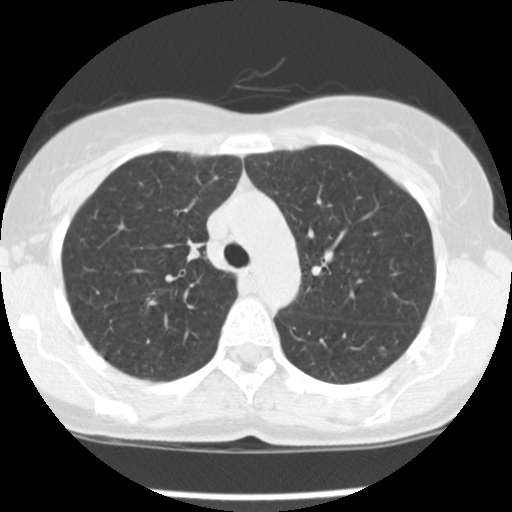
Low-dose screening chest CT, one axial slice. Reconstruction kernel STANDARD. Lung window (W 1500 / L -600 HU). 2.5 mm slice thickness. 512 × 512 image matrix, field of view 282 × 282 mm.
Annotated regions visible in this slice (expert manual segmentation):
- lesion 1 (tumor, upper lobe of right lung): box from (x=187, y=240) to (x=204, y=261) px